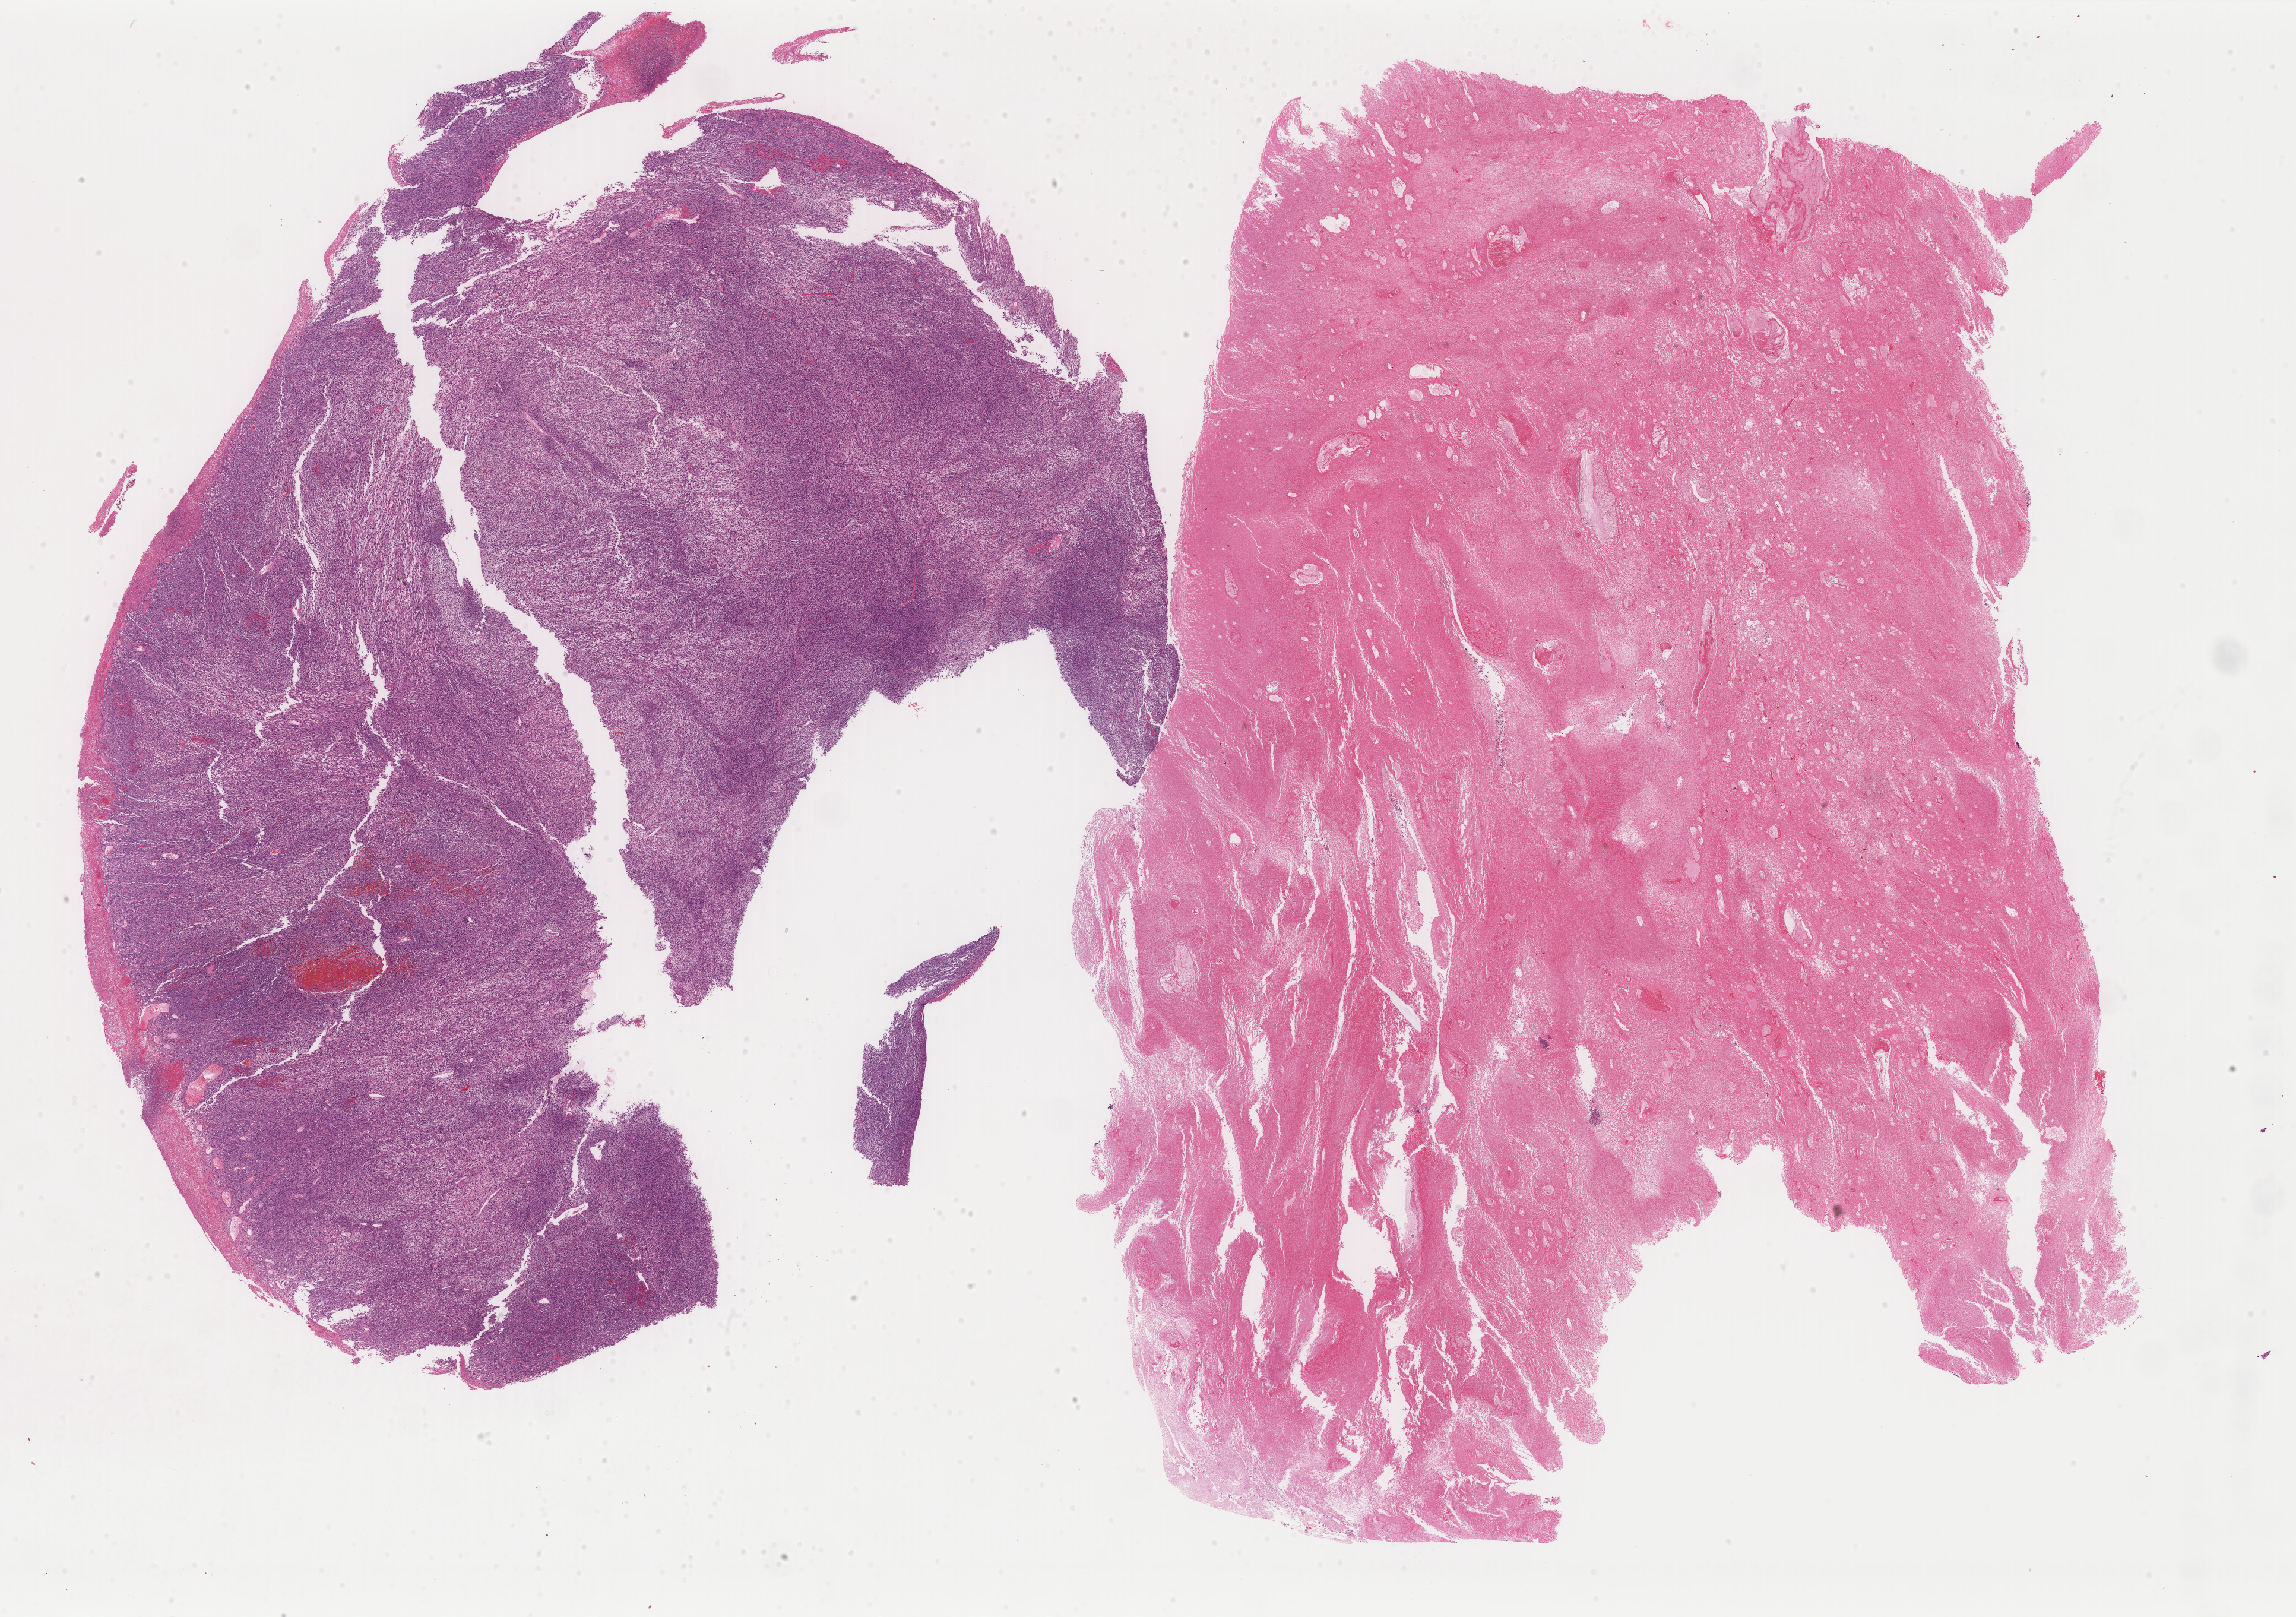
H&E-stained whole-slide image, a low-resolution overview of the entire scanned area, about 30.7 x 21.6 mm (slide scanned at 40x). Formalin-fixed paraffin-embedded (FFPE) diagnostic section. Uterus, primary tumour sample. Female, age 77 years at initial diagnosis.
* diagnosis: Mullerian mixed tumor (fundus uteri)
* FIGO stage: IIIA